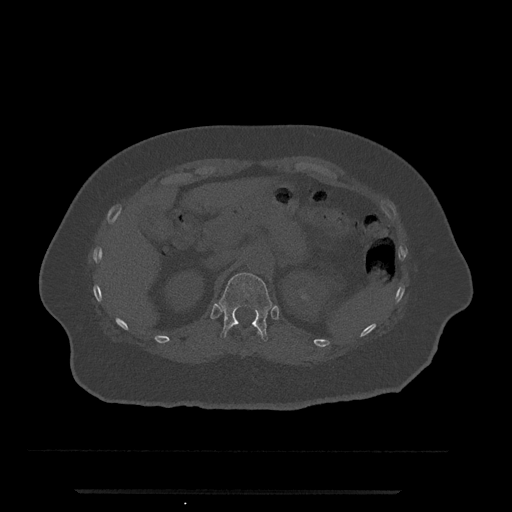
CT including the spine, one axial slice; 120 kVp; bone window (W 1800 / L 400 HU); 0.5 mm slice thickness; 512 × 512 image matrix, field of view 440 × 440 mm. Patient: female, 51 years. From the clinical record (not read from this slice): primary cancer: neuro; vertebrae with lytic lesions (as recorded): T8.
Annotated regions visible in this slice (semi-automatically segmented with operator editing):
- T11 vertebra: bounding box <257,331,261,335> (left, top, right, bottom; pixels)
- T12 vertebra: <219,273,273,342>